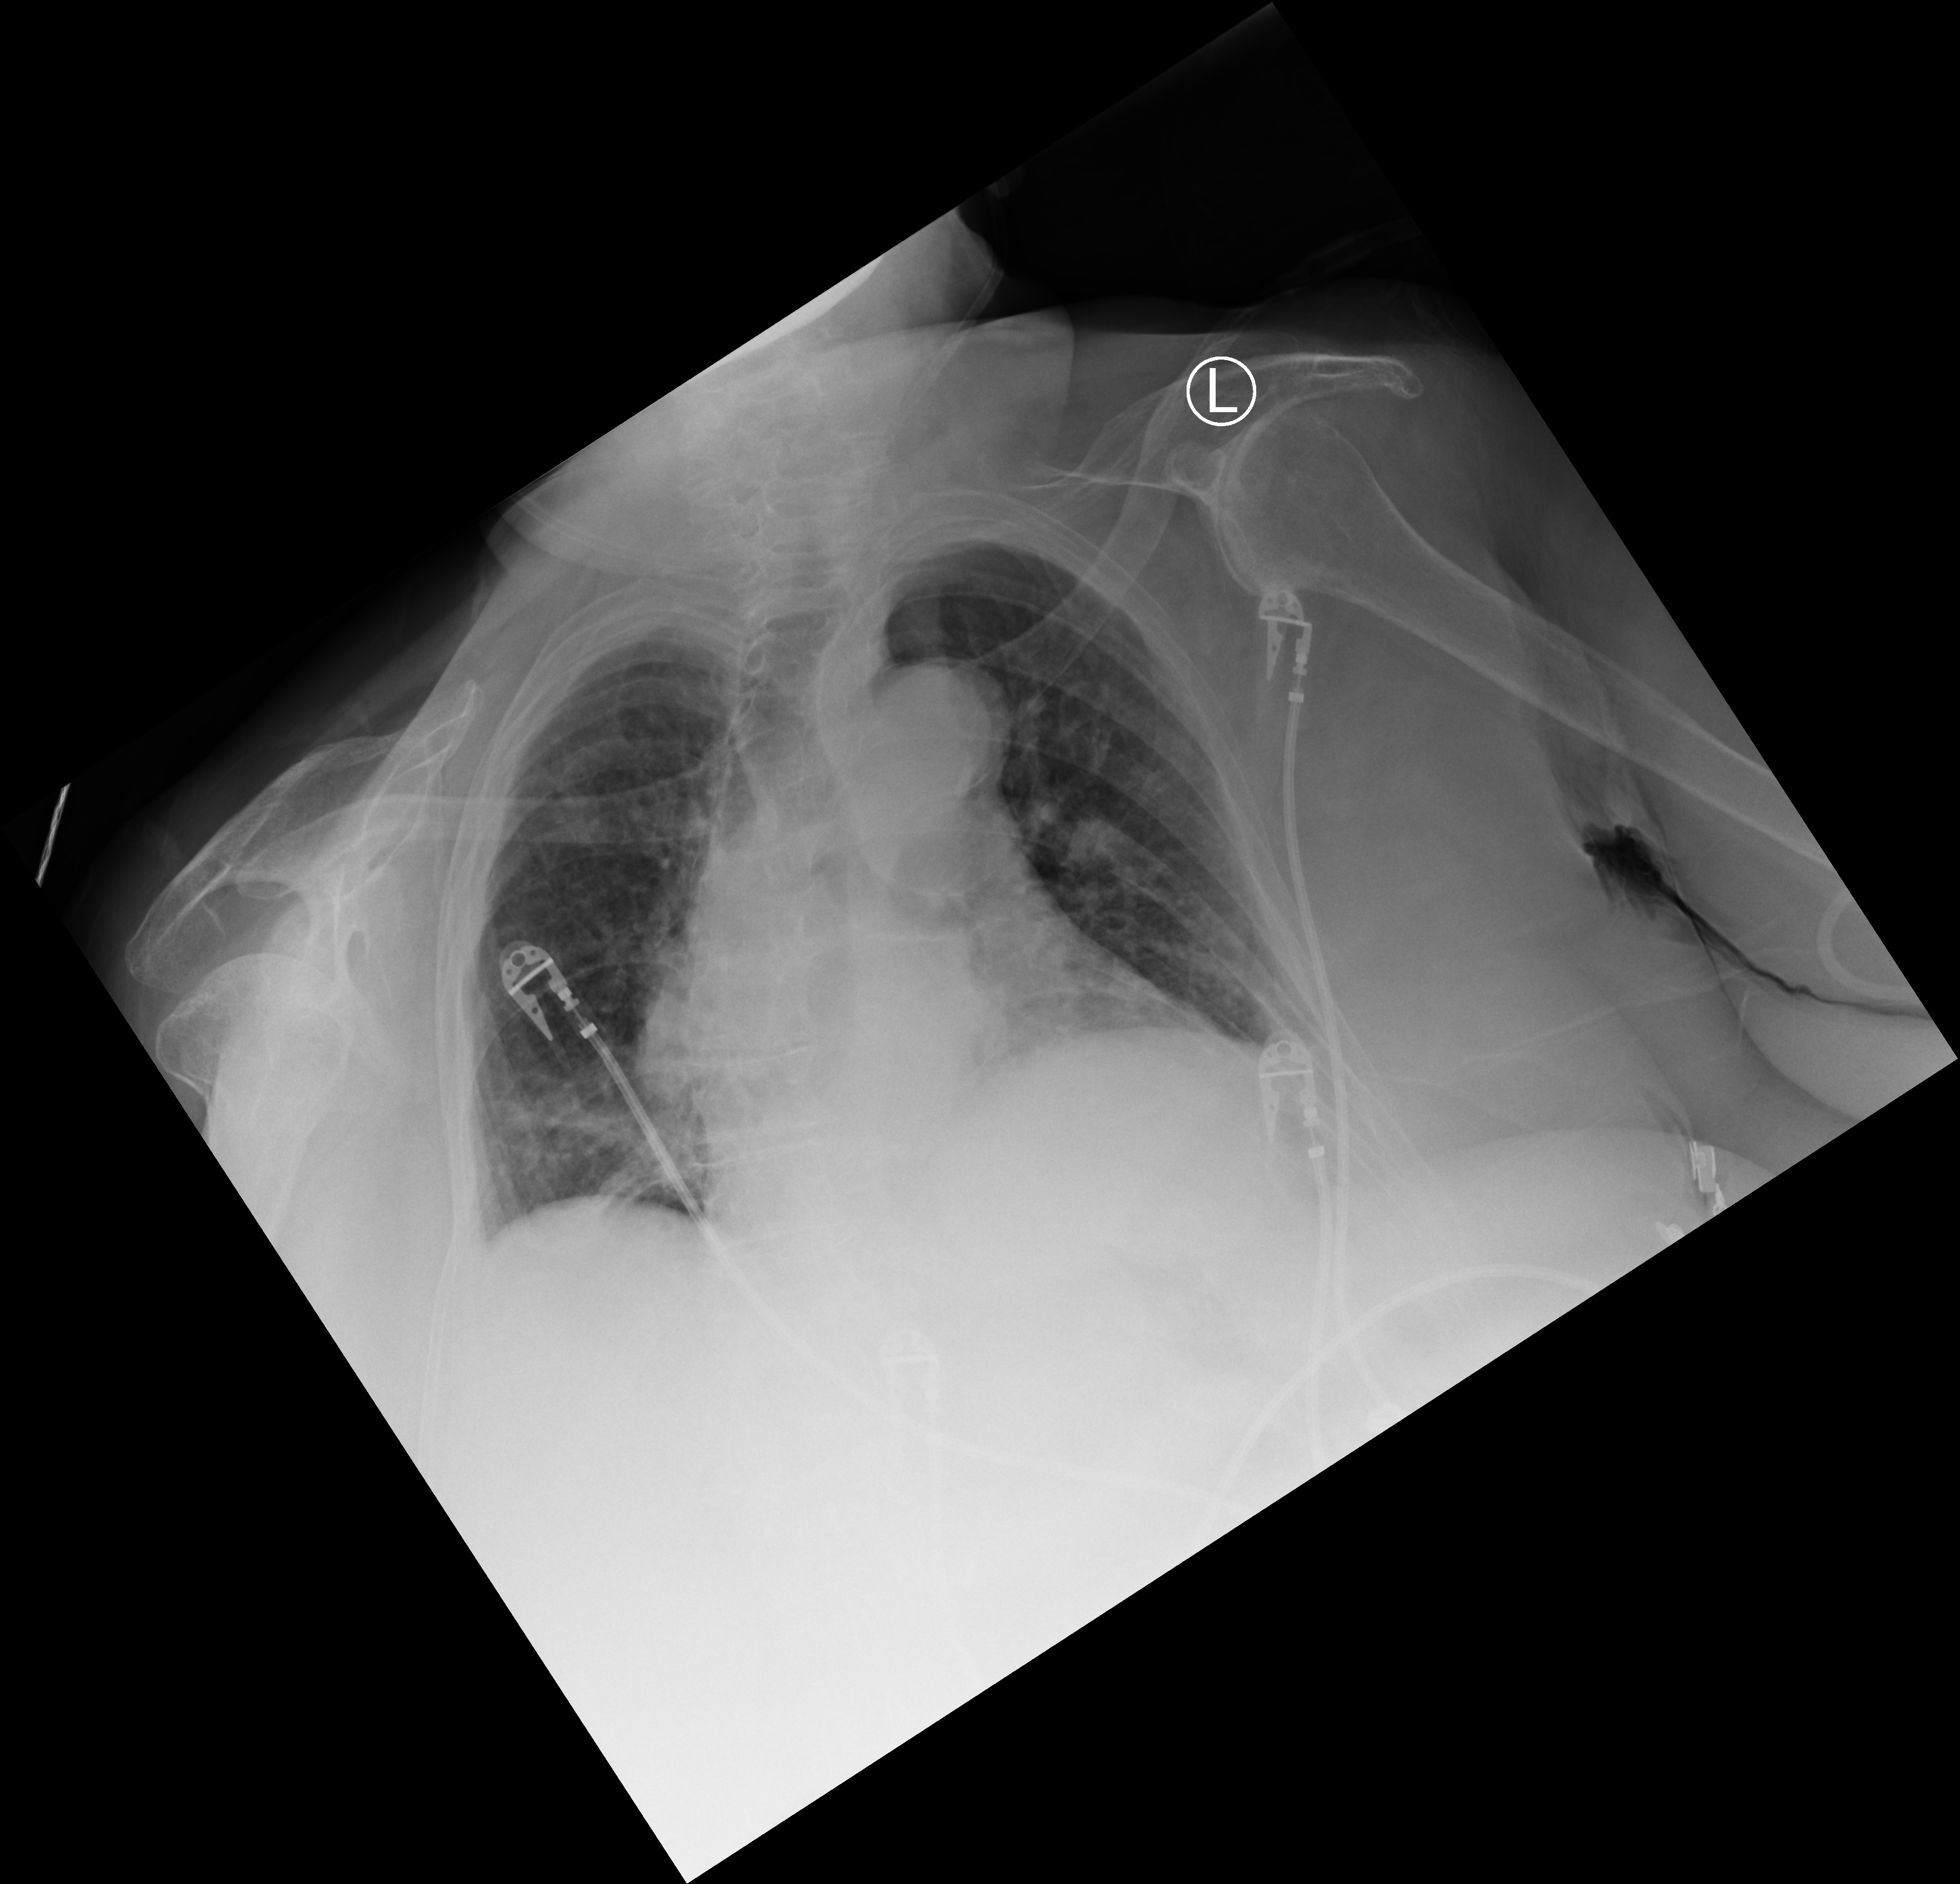
Portable chest radiograph, anteroposterior (AP) projection. Patient hospitalised with COVID-19; female, aged 75–90 years.
From the hospital-stay record, not from the radiograph (when in the stay this image was taken is not recorded):
- admitted to intensive care during this hospital stay: yes
- length of hospital stay: 12 days